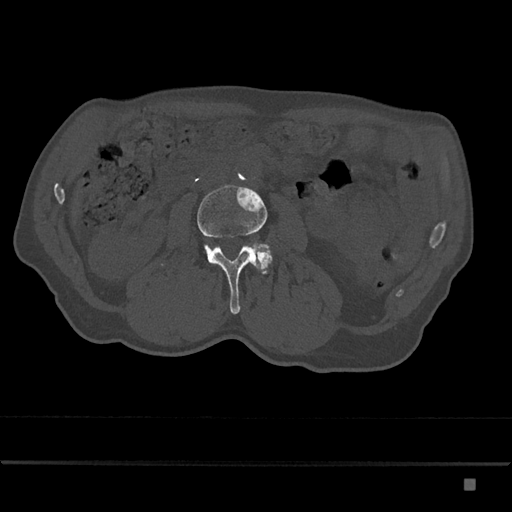
CT including the spine, one axial slice. Slice 399 of 797 in the series (ordered by position). Reconstruction kernel Br40s/3. 120 kVp. Bone window (W 1800 / L 400 HU). 0.5 mm slice thickness. 512 × 512 image matrix, field of view 390 × 390 mm. Male patient, age 72 years. From the clinical record (not read from this slice): primary cancer: prostate.
Annotated regions visible in this slice (semi-automatically segmented with operator editing):
- L3 vertebra: bounding box (x1, y1, x2, y2) in pixels: (161, 185, 270, 314)
- L4 vertebra: (255, 246, 272, 274)